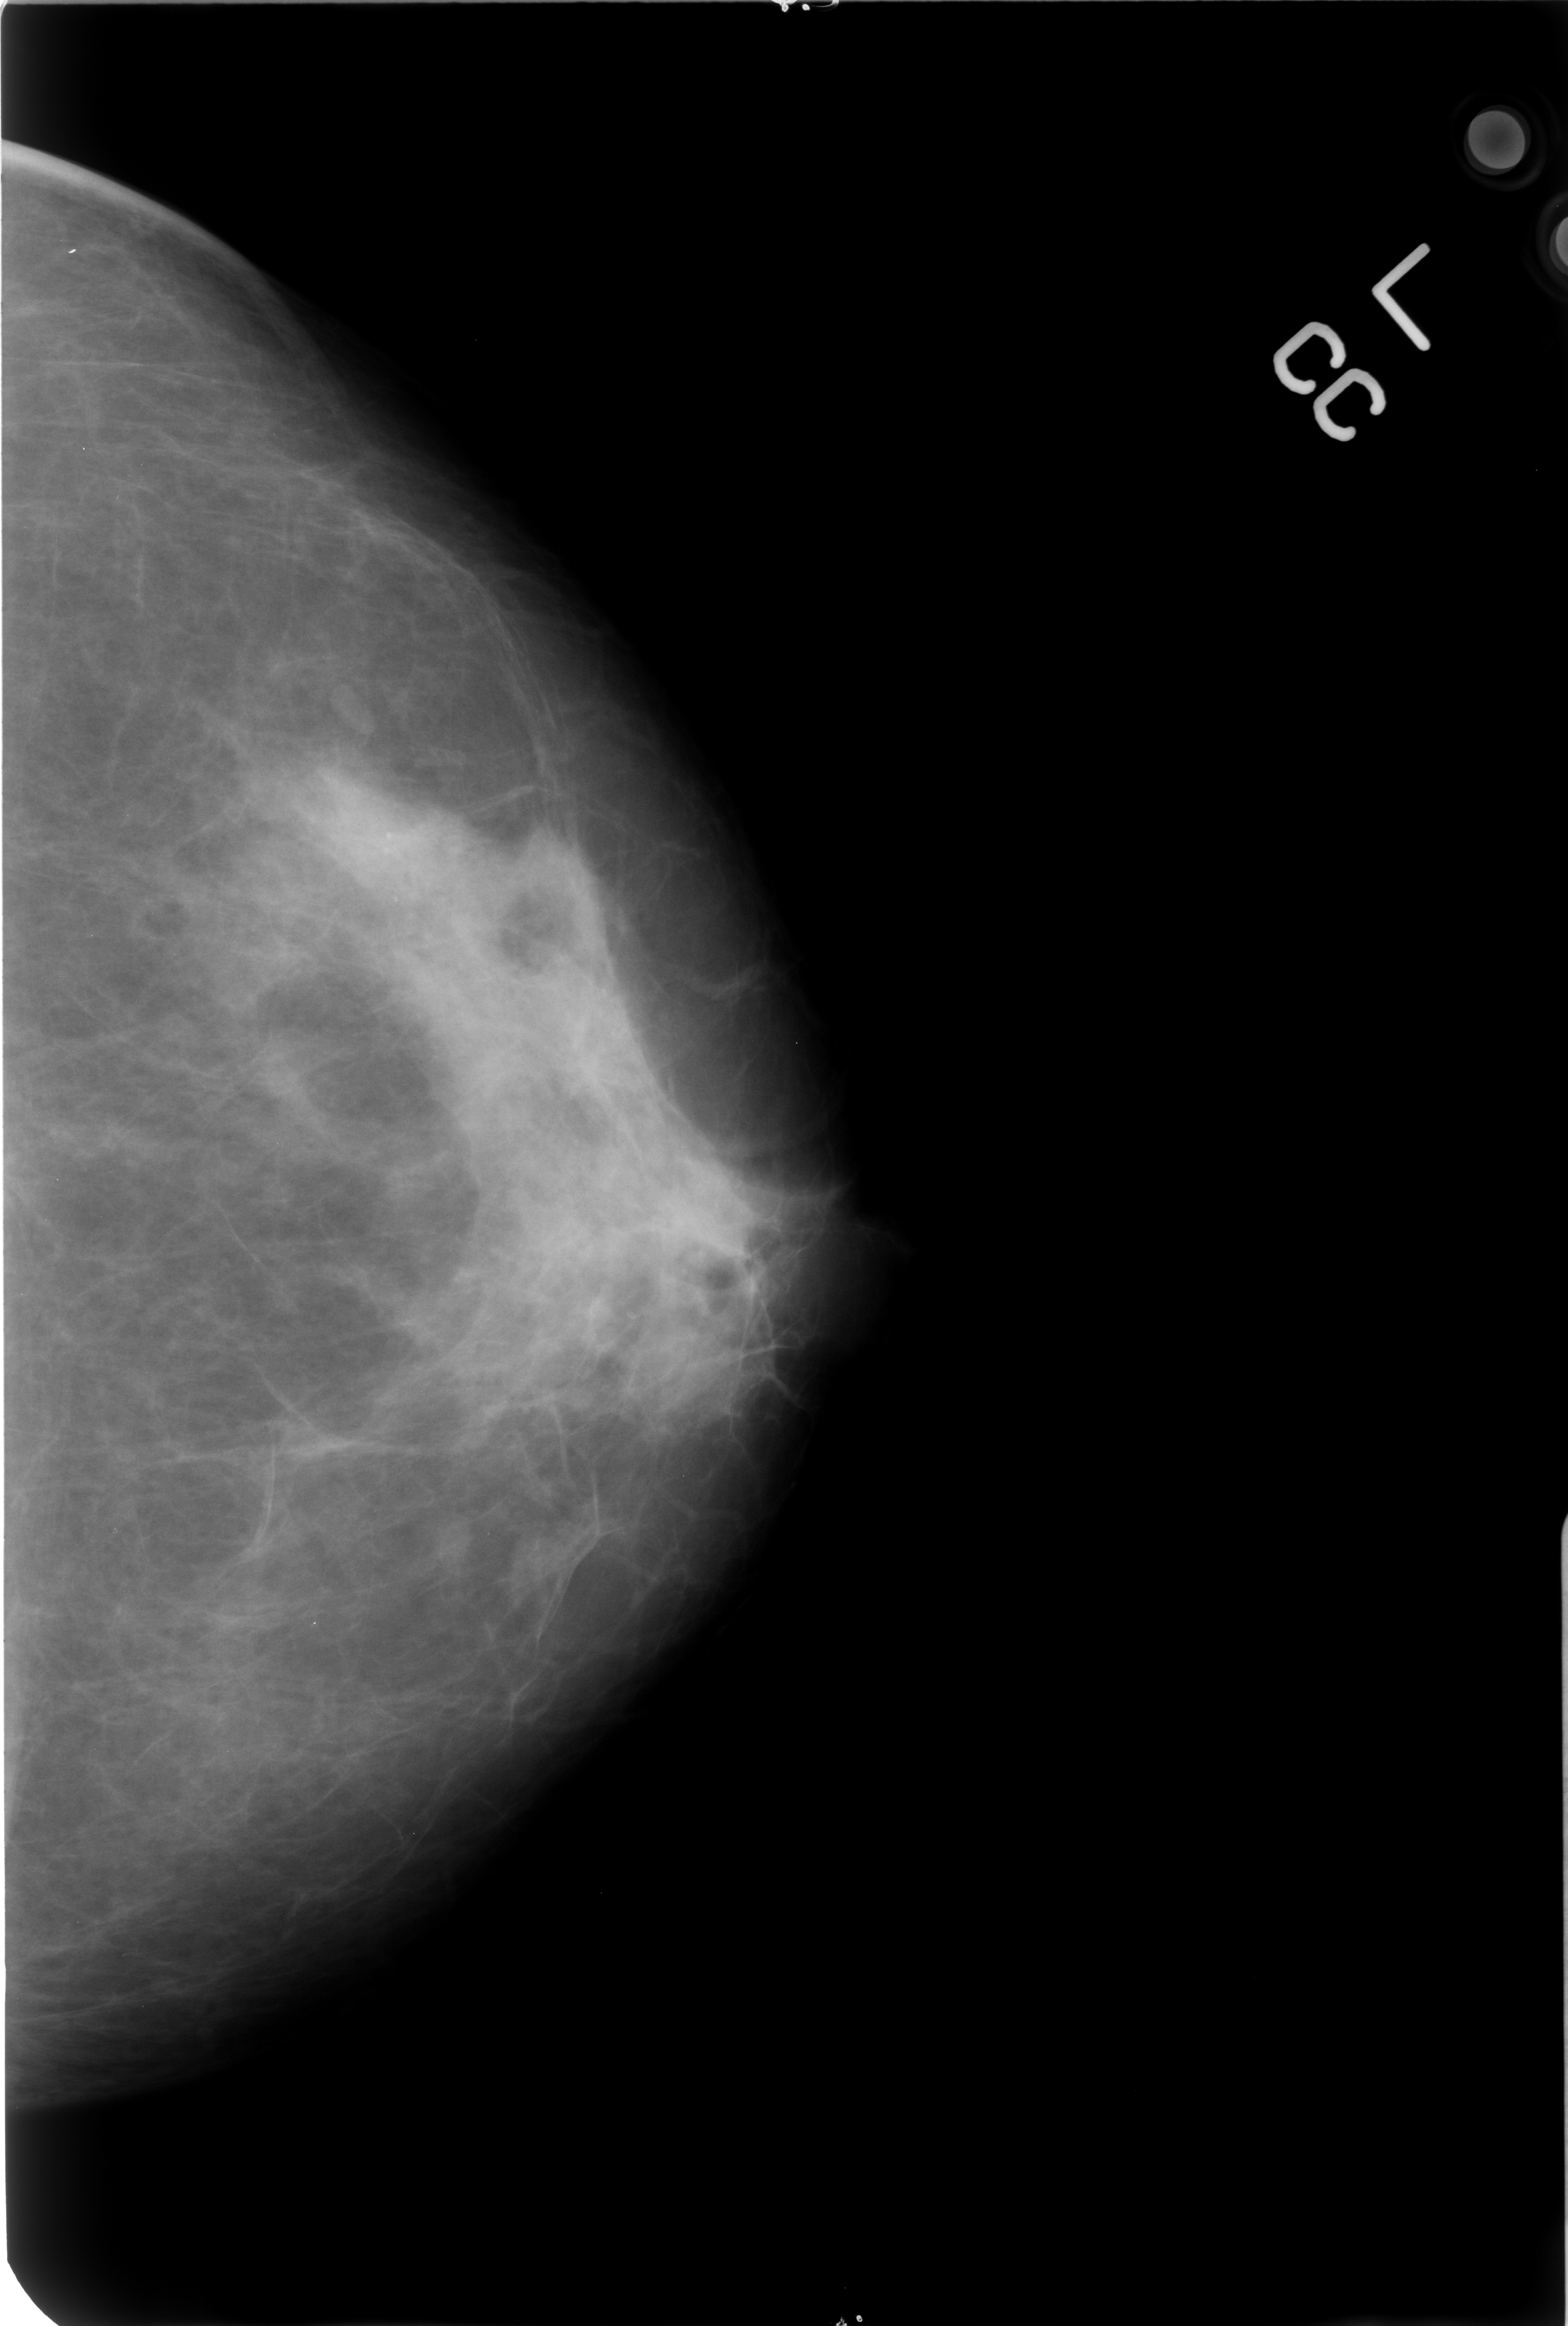
Mammogram (digitized film); left breast; craniocaudal (CC) view; BI-RADS breast density category 3 (scale 1–4); 1568 × 2326 image matrix.
Marked abnormalities (boxes around the expert regions of interest):
- calcifications, morphology punctate, distribution clustered; BI-RADS assessment category 2; benign; no additional work-up was recommended (outcome (as recorded, no biopsy): benign without callback): box from (x=286, y=753) to (x=509, y=916) px